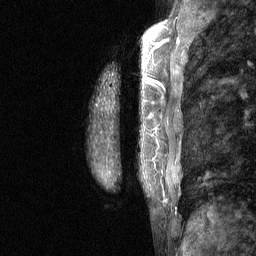
Breast MRI (dynamic contrast-enhanced), one sagittal slice. Slice 17 of 64 in the series (ordered by position). Dynamic contrast-enhanced study with each time point stored as its own series, time point 2 of 3 at this slice position (early post-contrast, ordered by acquisition time). 1.5 T. TE 4.8 ms, TR 27 ms. 2 mm slice thickness. 256 × 256 image matrix, field of view 180 × 180 mm. Patient: female, 36 years. Case-level facts recorded for this patient, not image findings: setting: breast cancer imaged before/during neoadjuvant chemotherapy; receptor status: HR-positive, HER2-negative.
Annotated regions visible in this slice (semi-automatic segmentation, software-assisted and operator-edited):
- analysis volume of interest (the breast-tissue region the enhancement analysis was run in; not a lesion): bounding box [x1, y1, x2, y2] px = [92, 12, 211, 236]
- tumour enhancement mask (voxels above the 90 % enhancement threshold inside the analysis volume of interest): [149, 37, 179, 86]